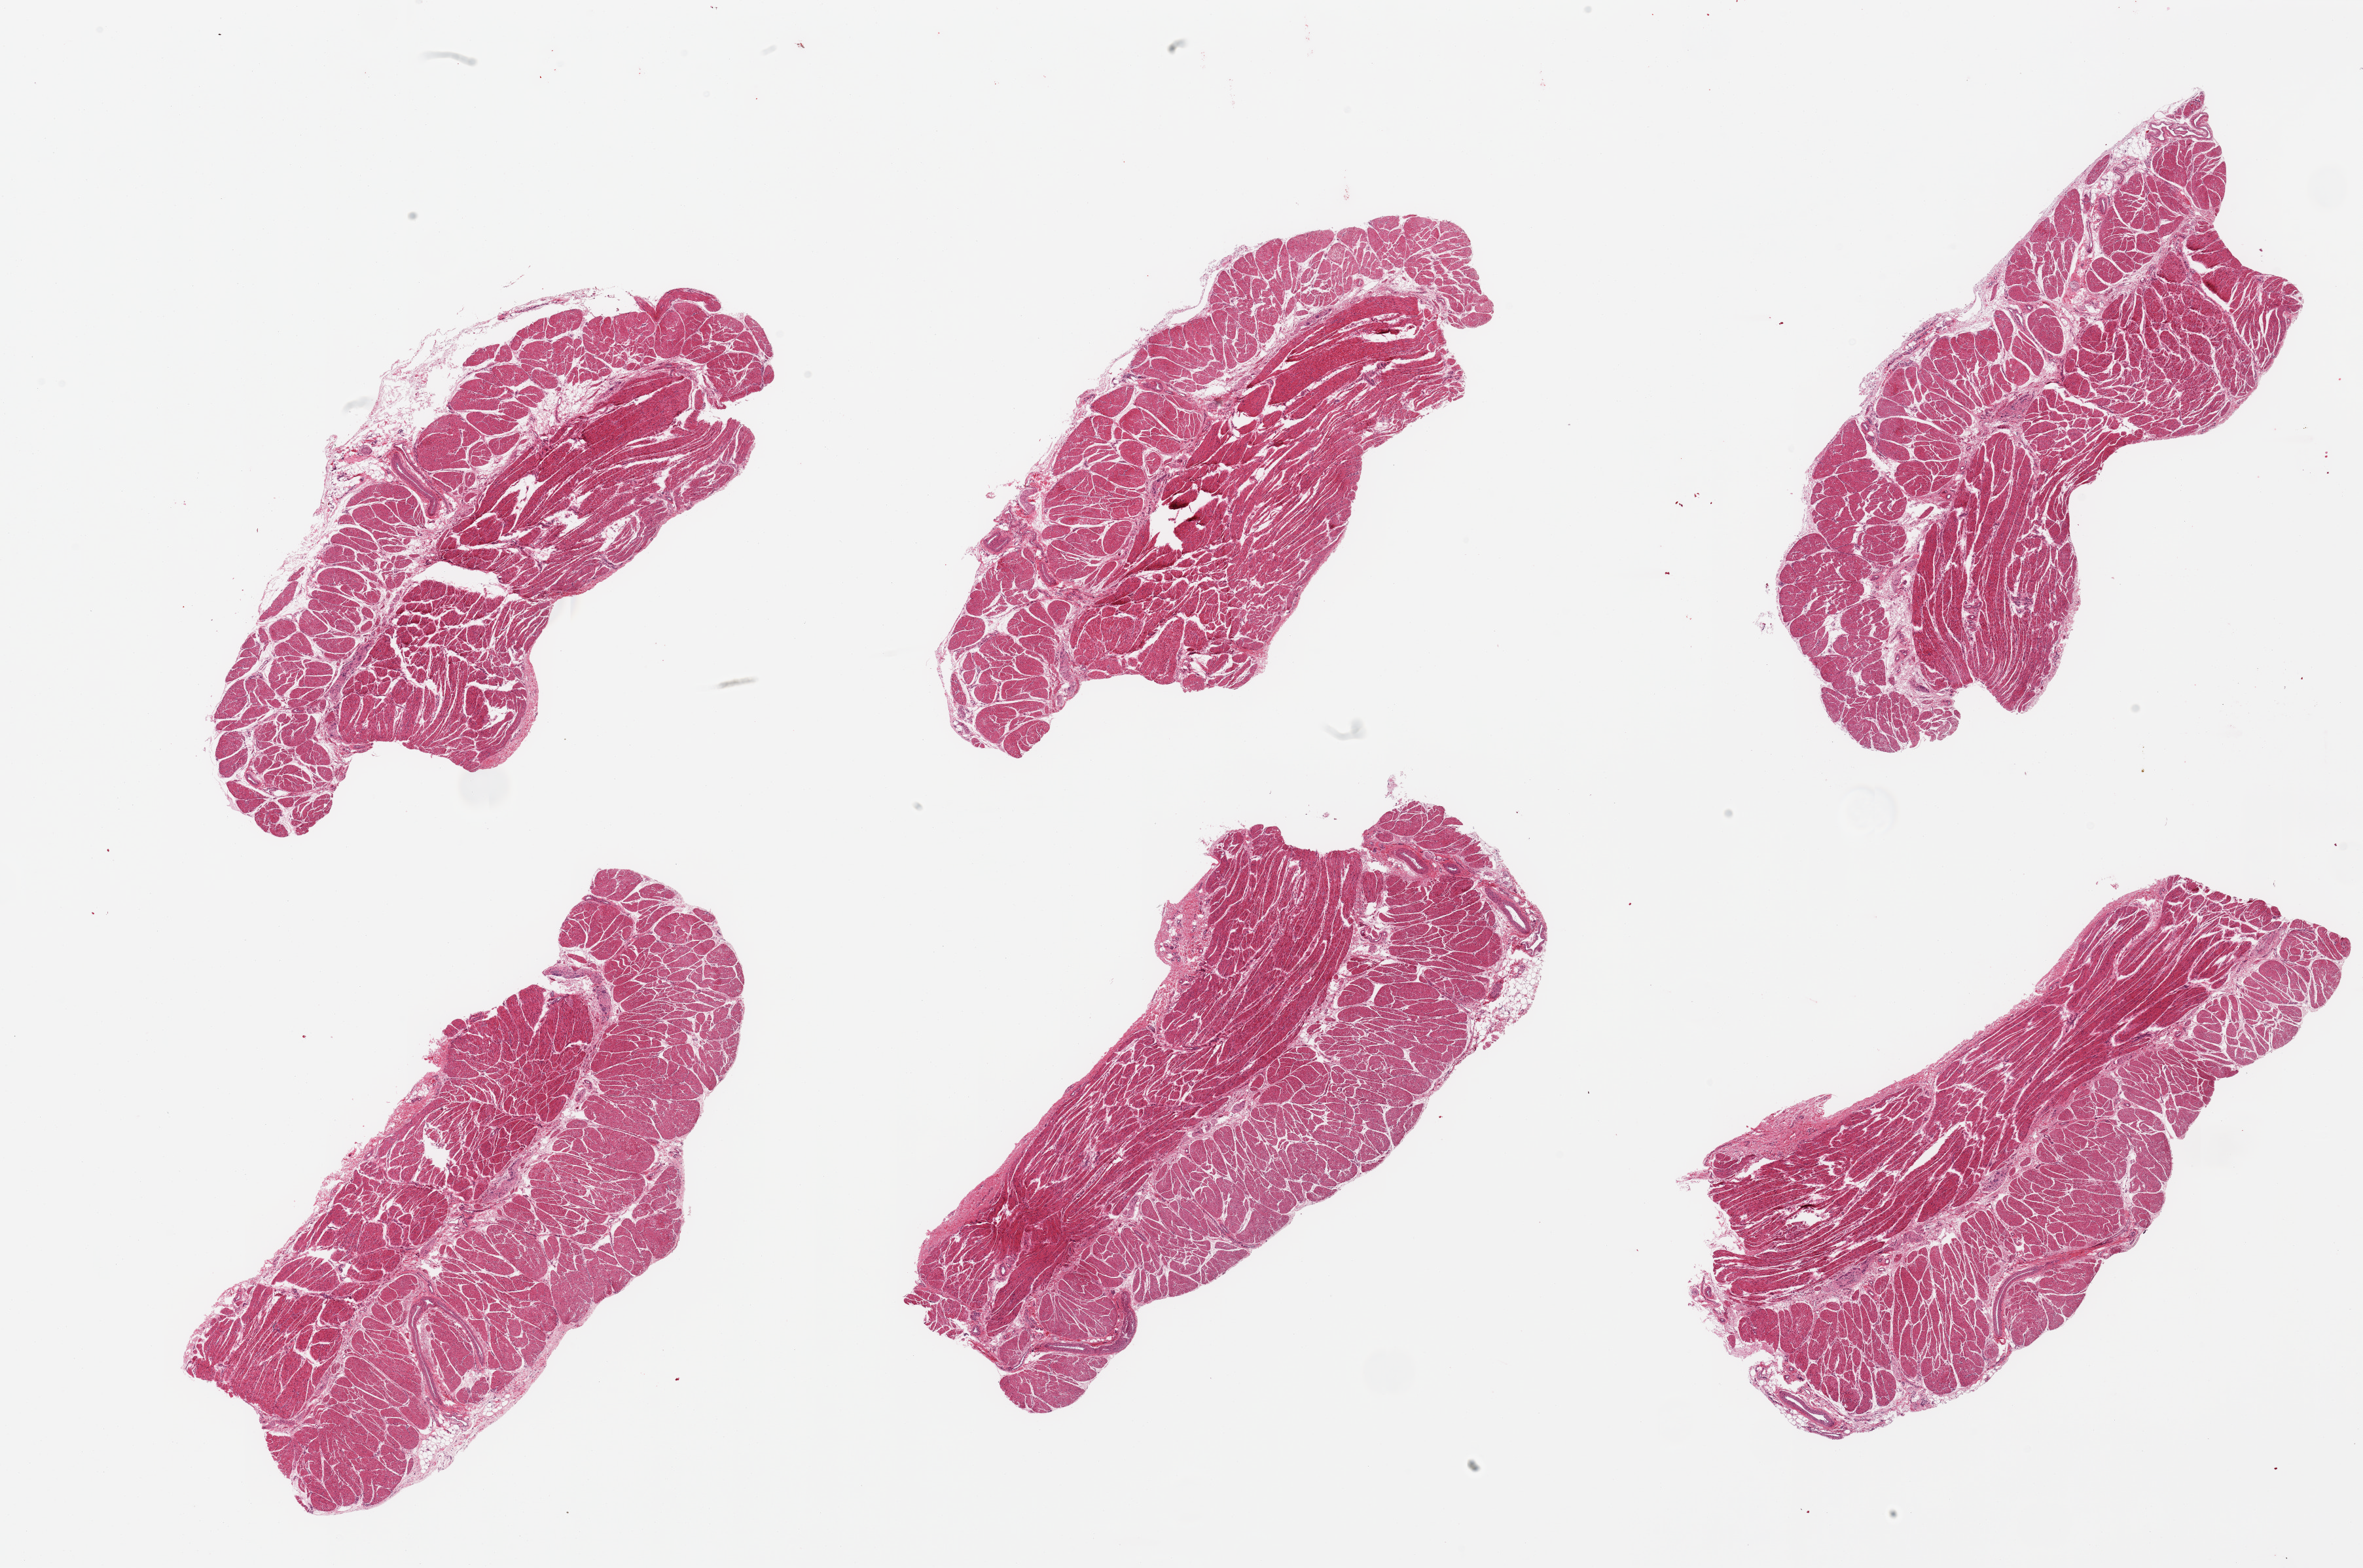
Whole-slide image, H&E stain — whole scanned area (about 28.5 x 18.9 mm) shown as a low-resolution overview; PAXgene-fixed, paraffin-embedded tissue; target tissue: gastroesophageal junction; tissue donor sample. Donor sex: male.
• reviewer comment on this tissue sample: 6 pieces; well trimmed